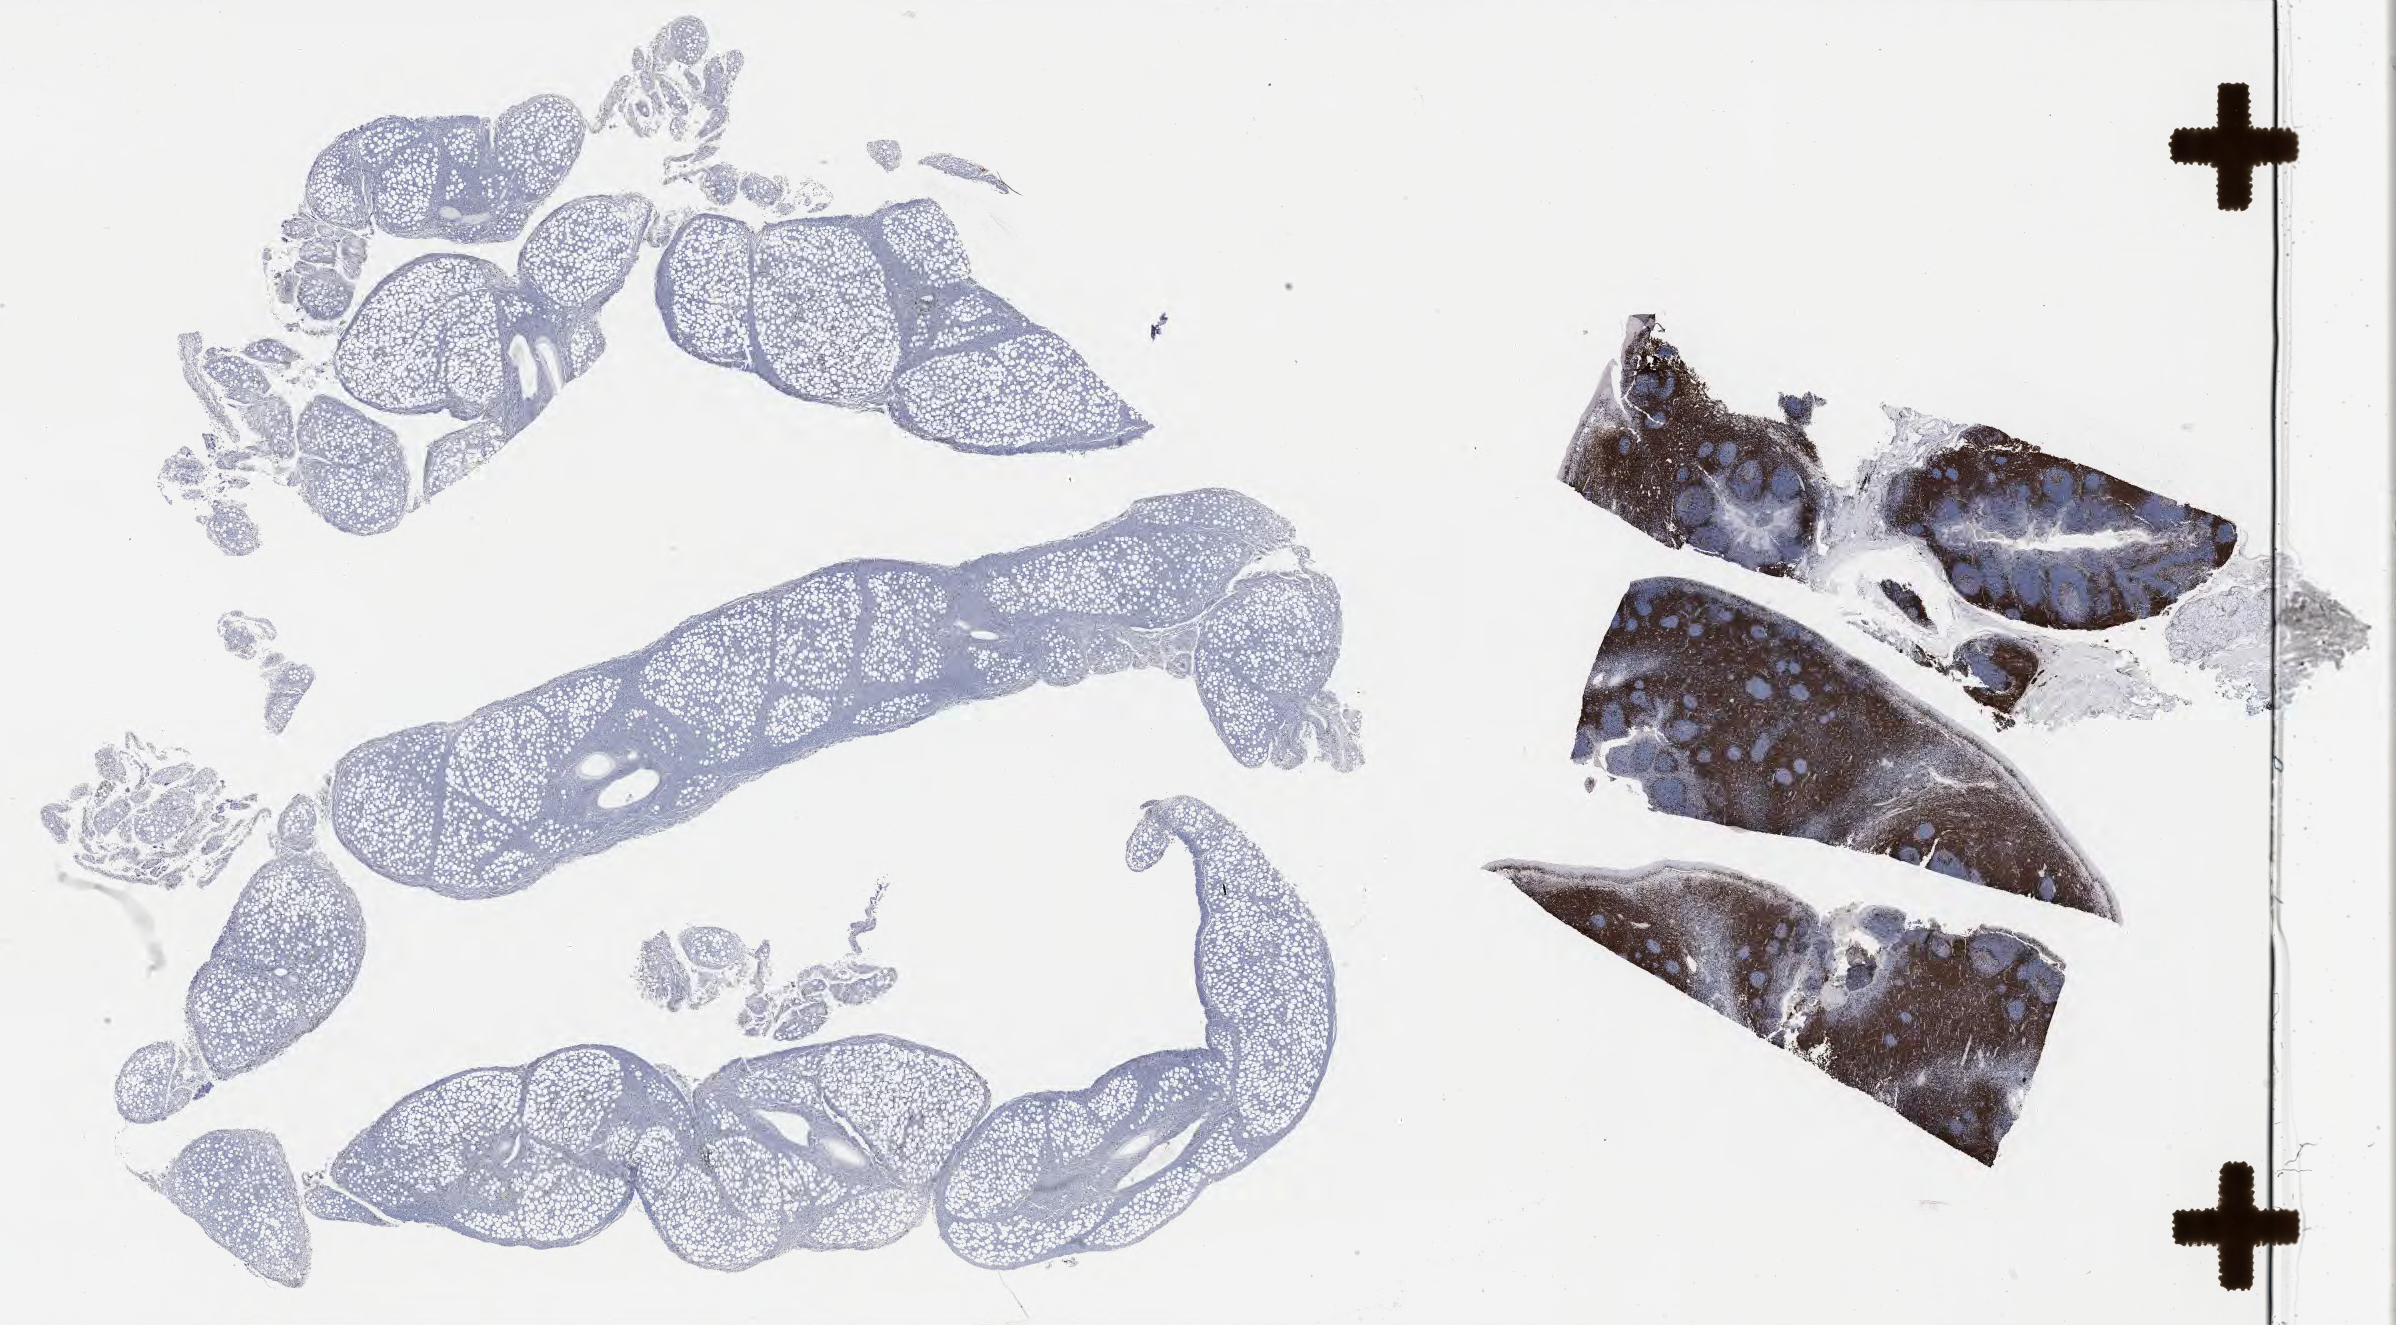
Immunohistochemistry (IHC) whole-slide image stained for CD3 — whole scanned area (about 38.8 x 21.4 mm) shown as a low-resolution overview. Tumor tissue. Anatomic site: abdomen proper. Patient: female, age at initial diagnosis 9 years.
* histologic diagnosis: Burkitt lymphoma, NOS